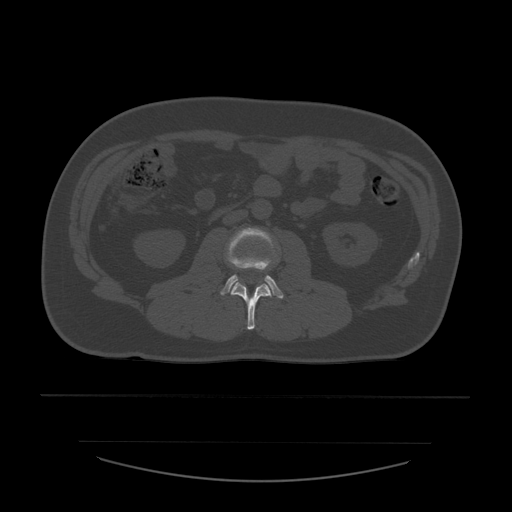
CT including the spine, one axial slice; slice 187 of 532 in the series (ordered by position); bone window (W 1800 / L 400 HU); 1.25 mm slice thickness; 512 × 512 image matrix, field of view 441 × 441 mm. Patient age 44 years. From the clinical record (not read from this slice): primary cancer: soft tissue sarcoma.
Annotated regions visible in this slice (semi-automatic segmentation, software-assisted and operator-edited):
- L2 vertebra: bounding box (x1, y1, x2, y2) in pixels: (231, 282, 272, 330)
- L3 vertebra: (221, 228, 284, 299)